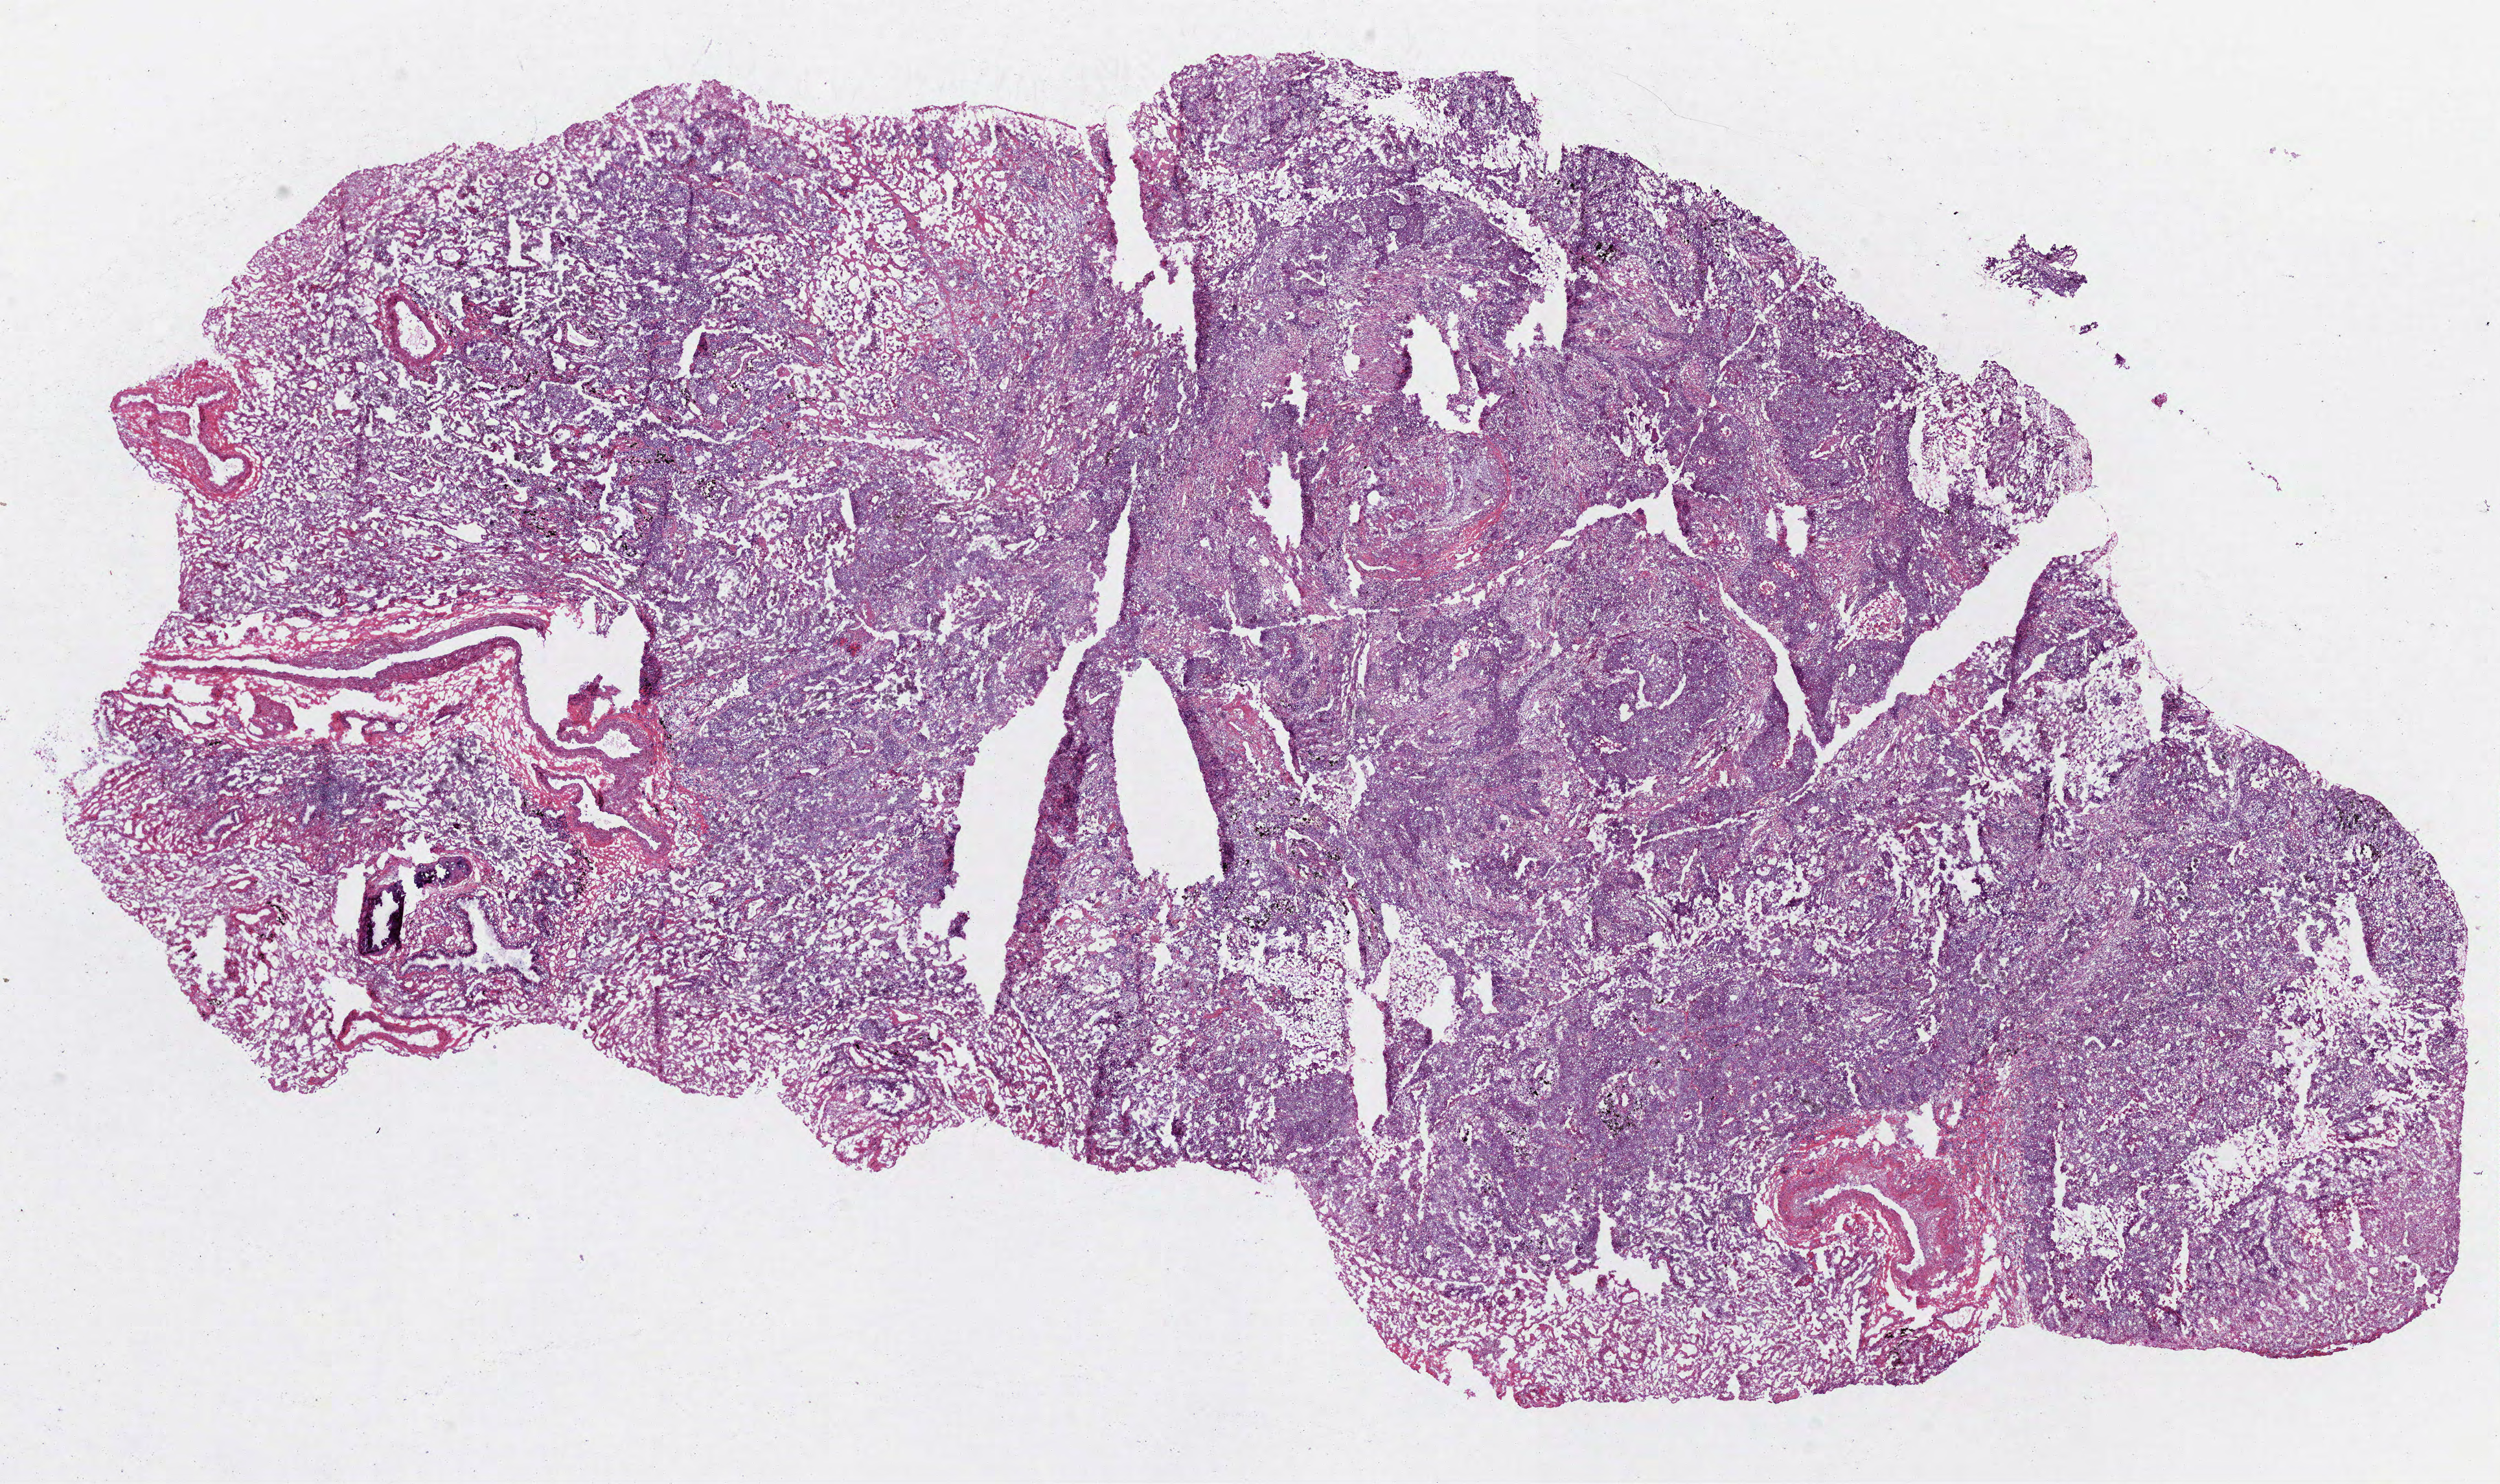
H&E whole-slide image, low-resolution overview of the scanned area, about 15.6 x 9.2 mm; frozen section from the bottom of the tissue portion; lung, primary tumour sample. Male patient; age at initial diagnosis 61 years. Composition of this section per pathologist review: tumour cells 75%, tumour nuclei 70%, normal cells 15%, stromal cells 10%, necrosis 0%.
AJCC pathologic stage: IA (7th edition). Laterality: right. Histologic diagnosis: Squamous cell carcinoma, NOS (upper lobe, lung).